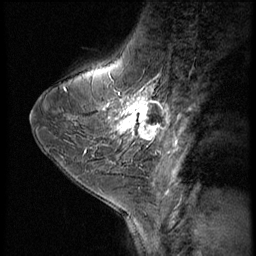
Breast MRI (dynamic contrast-enhanced), one sagittal slice. Position 19 of 56 along the scan axis. Dynamic contrast-enhanced series, image 2 of 3 at this slice position (ordered by acquisition). 1.5 T. TE 4.2 ms, TR 9 ms. 256 × 256 image matrix, field of view 180 × 180 mm. Patient: female, 38 years. From the clinical record (not read from this slice): setting: breast cancer imaged before/during neoadjuvant chemotherapy; receptor status: triple-negative.
Outlined on this slice (semi-automatic segmentation, software-assisted and operator-edited):
- analysis volume of interest (the breast-tissue region the enhancement analysis was run in; not a lesion): bounding box (x1, y1, x2, y2) in pixels: (107, 95, 172, 149)
- tumour enhancement mask (voxels above the 140 % enhancement threshold inside the analysis volume of interest): (115, 95, 169, 140)